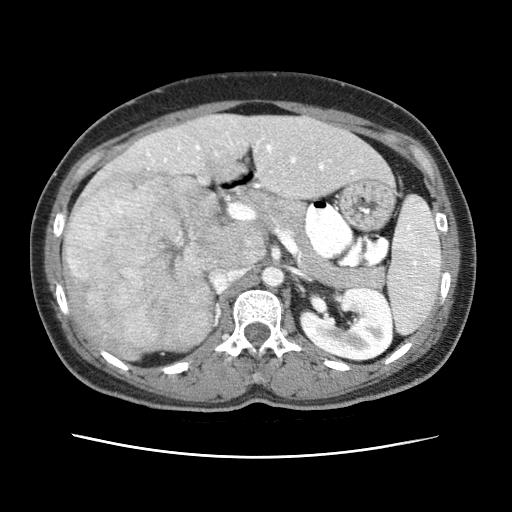
Contrast-enhanced abdominal CT (liver protocol), one axial slice. Position 27 of 79 along the scan axis. Reconstruction kernel STANDARD. 120 kVp. Soft-tissue window (W 400 / L 40 HU). 2.5 mm slice thickness. 512 × 512 image matrix, field of view 340 × 340 mm. From the clinical record (not read from this slice): diagnosis: hepatocellular carcinoma (patient treated with transarterial chemoembolisation; whether this scan precedes or follows treatment is not stated here); TNM stage (as recorded): Stage-I; Child-Pugh class: A; tumour differentiation: moderately differentiated; tumour nodularity: uninodular.
Annotated regions visible in this slice (semi-automatically segmented with operator editing):
- abdominal aorta: box from (x=263, y=268) to (x=284, y=286) px
- liver parenchyma outside the tumour (the mass and vessels are separate outlines, so this box may not span the whole liver): (x=62, y=114)–(x=388, y=356)
- mass: (x=63, y=167)–(x=227, y=357)
- liver vessels: (x=147, y=145)–(x=354, y=174)